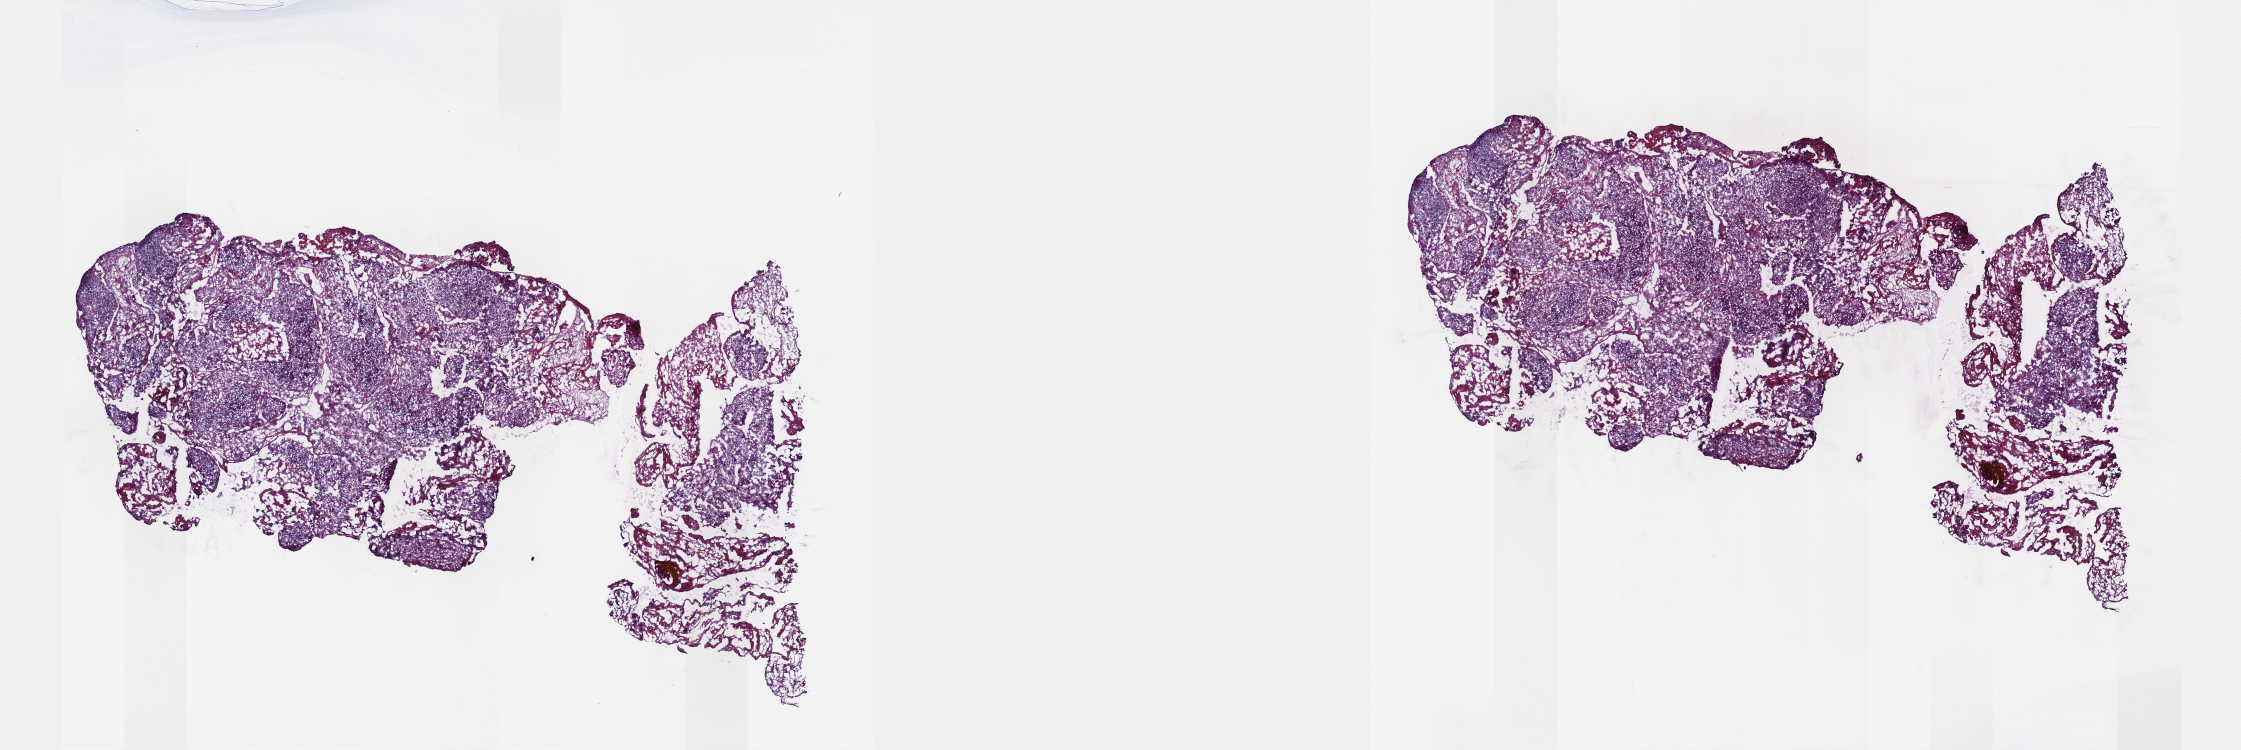
H&E-stained whole-slide image, low-resolution overview of the scanned area, about 18.1 x 6.1 mm, frozen section from the top of the tissue portion, primary tumour sample from the cervix. Patient: female, age at initial diagnosis 50 years. Histologic grade: G2 (moderately differentiated). Pathologist review of this section (percent, as recorded): tumour cells 80%, tumour nuclei 80%, normal cells 0%, stromal cells 18%, necrosis 2%. Infiltration values recorded for this section: lymphocyte infiltration 10%, monocyte infiltration 0%, neutrophil infiltration 0%.
* FIGO stage: IIIB
* diagnosis: Squamous cell carcinoma, NOS (cervix uteri)